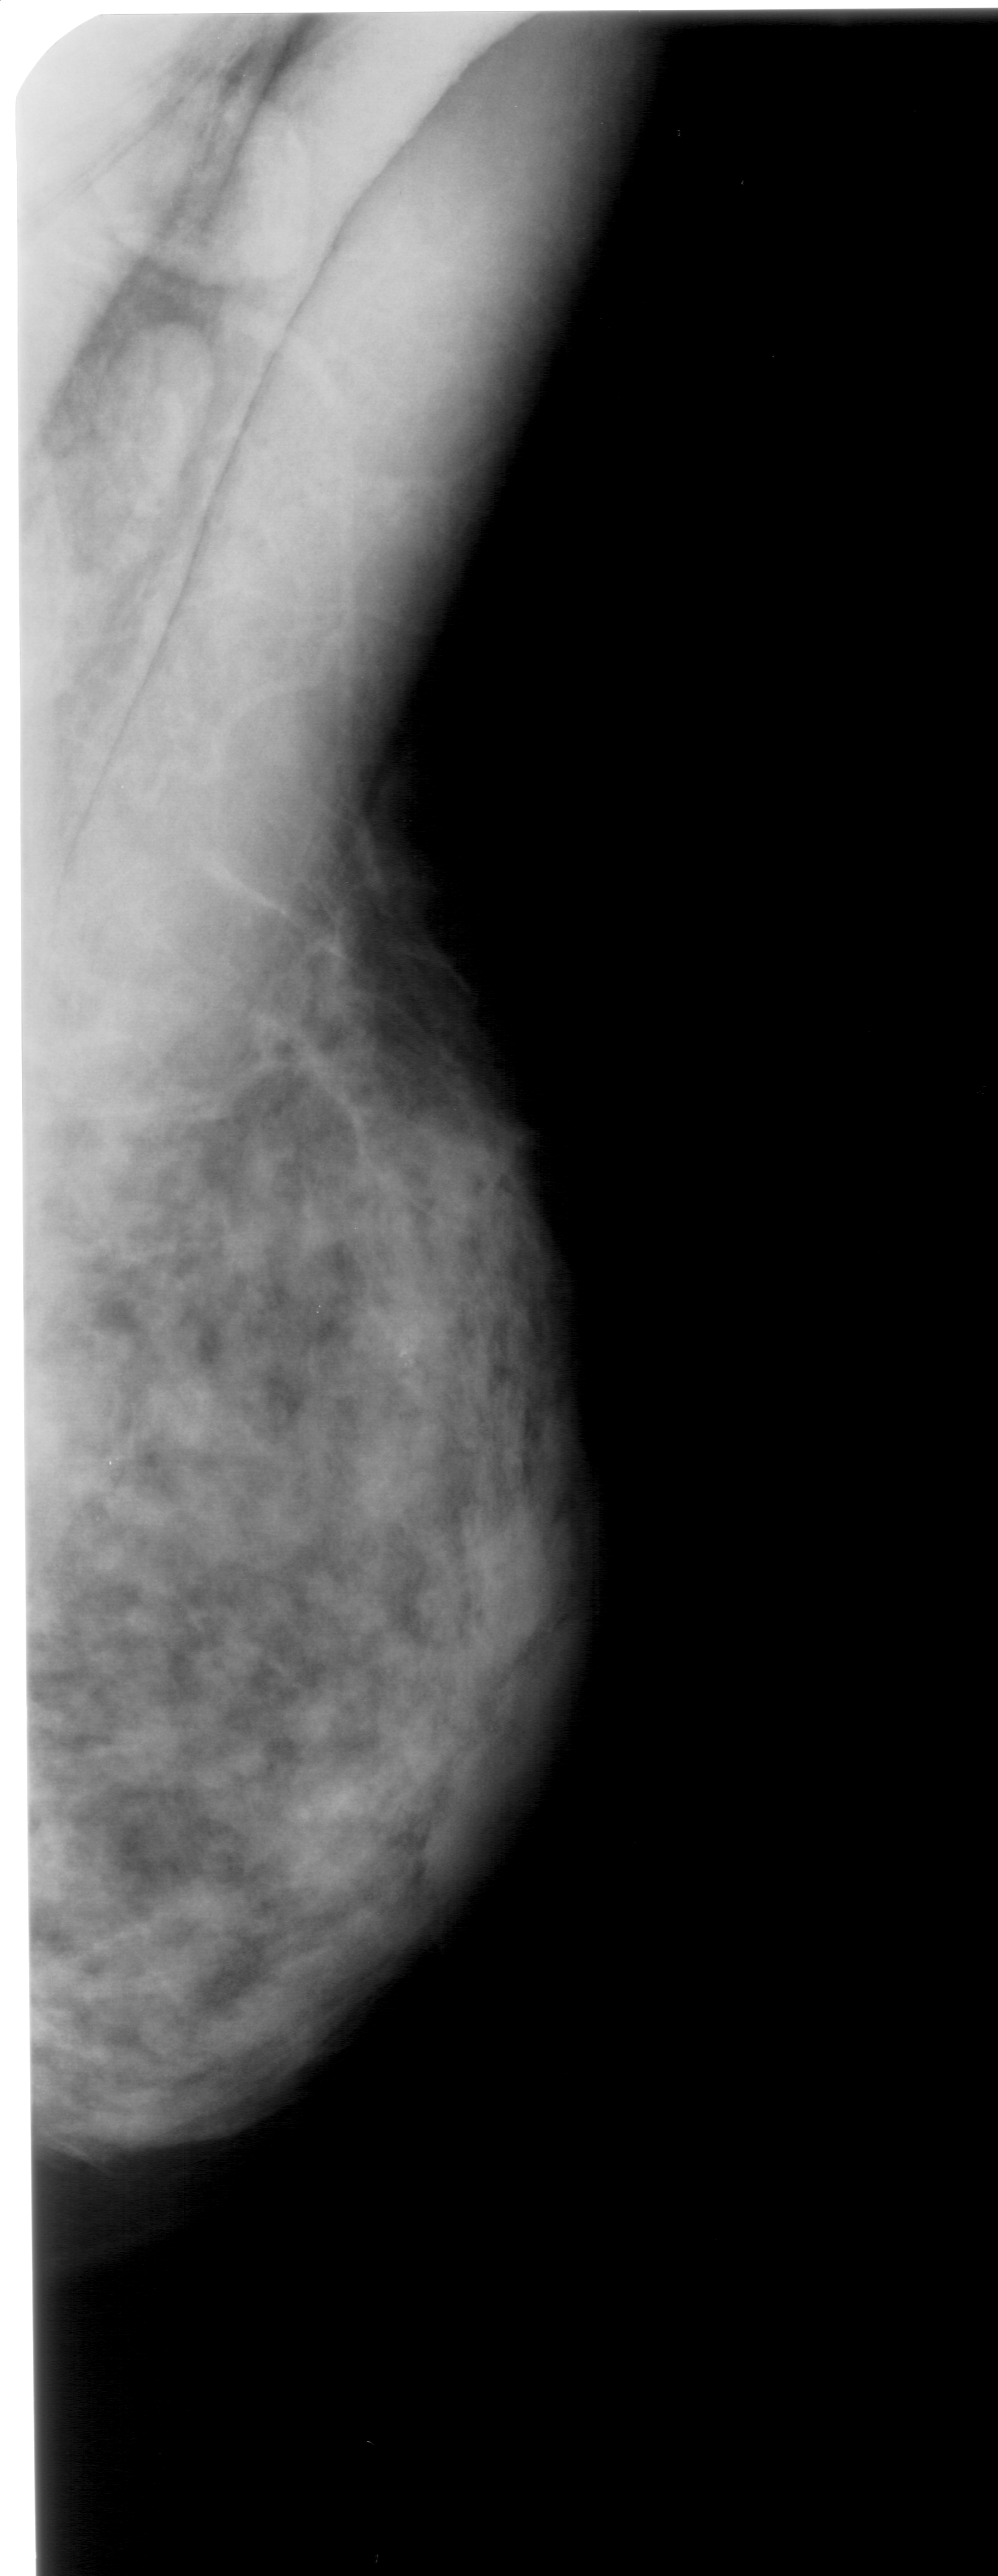
Scanned film-screen mammogram, right breast, mediolateral oblique (MLO) view, BI-RADS breast density category 3 (scale 1–4).
Marked abnormality: calcifications, morphology pleomorphic, distribution clustered; BI-RADS assessment category 4; pathology result (as recorded, not read from the image): benign.